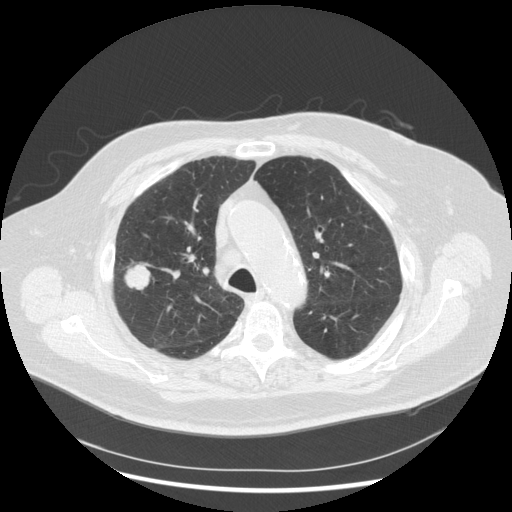
Low-dose screening chest CT, axial slice; third annual screen; lung window (W 1500 / L -600 HU); 2.5 mm slice thickness; standard (soft-tissue) reconstruction kernel (STANDARD); 120 kVp; slice 202 of 263 in the series; 512 × 512 image matrix. Male participant, aged 72 years at enrolment. Former smoker at enrolment.
Expert reader's lesion annotation, box from (x=109, y=252) to (x=162, y=302) px. Reader record for this screening exam (exam-level; its link to the box is not recorded): non-calcified nodule or mass ≥4 mm, right upper lobe, 31 × 31 mm, poorly defined margins, soft tissue attenuation, pre-existing on the prior screen: no.